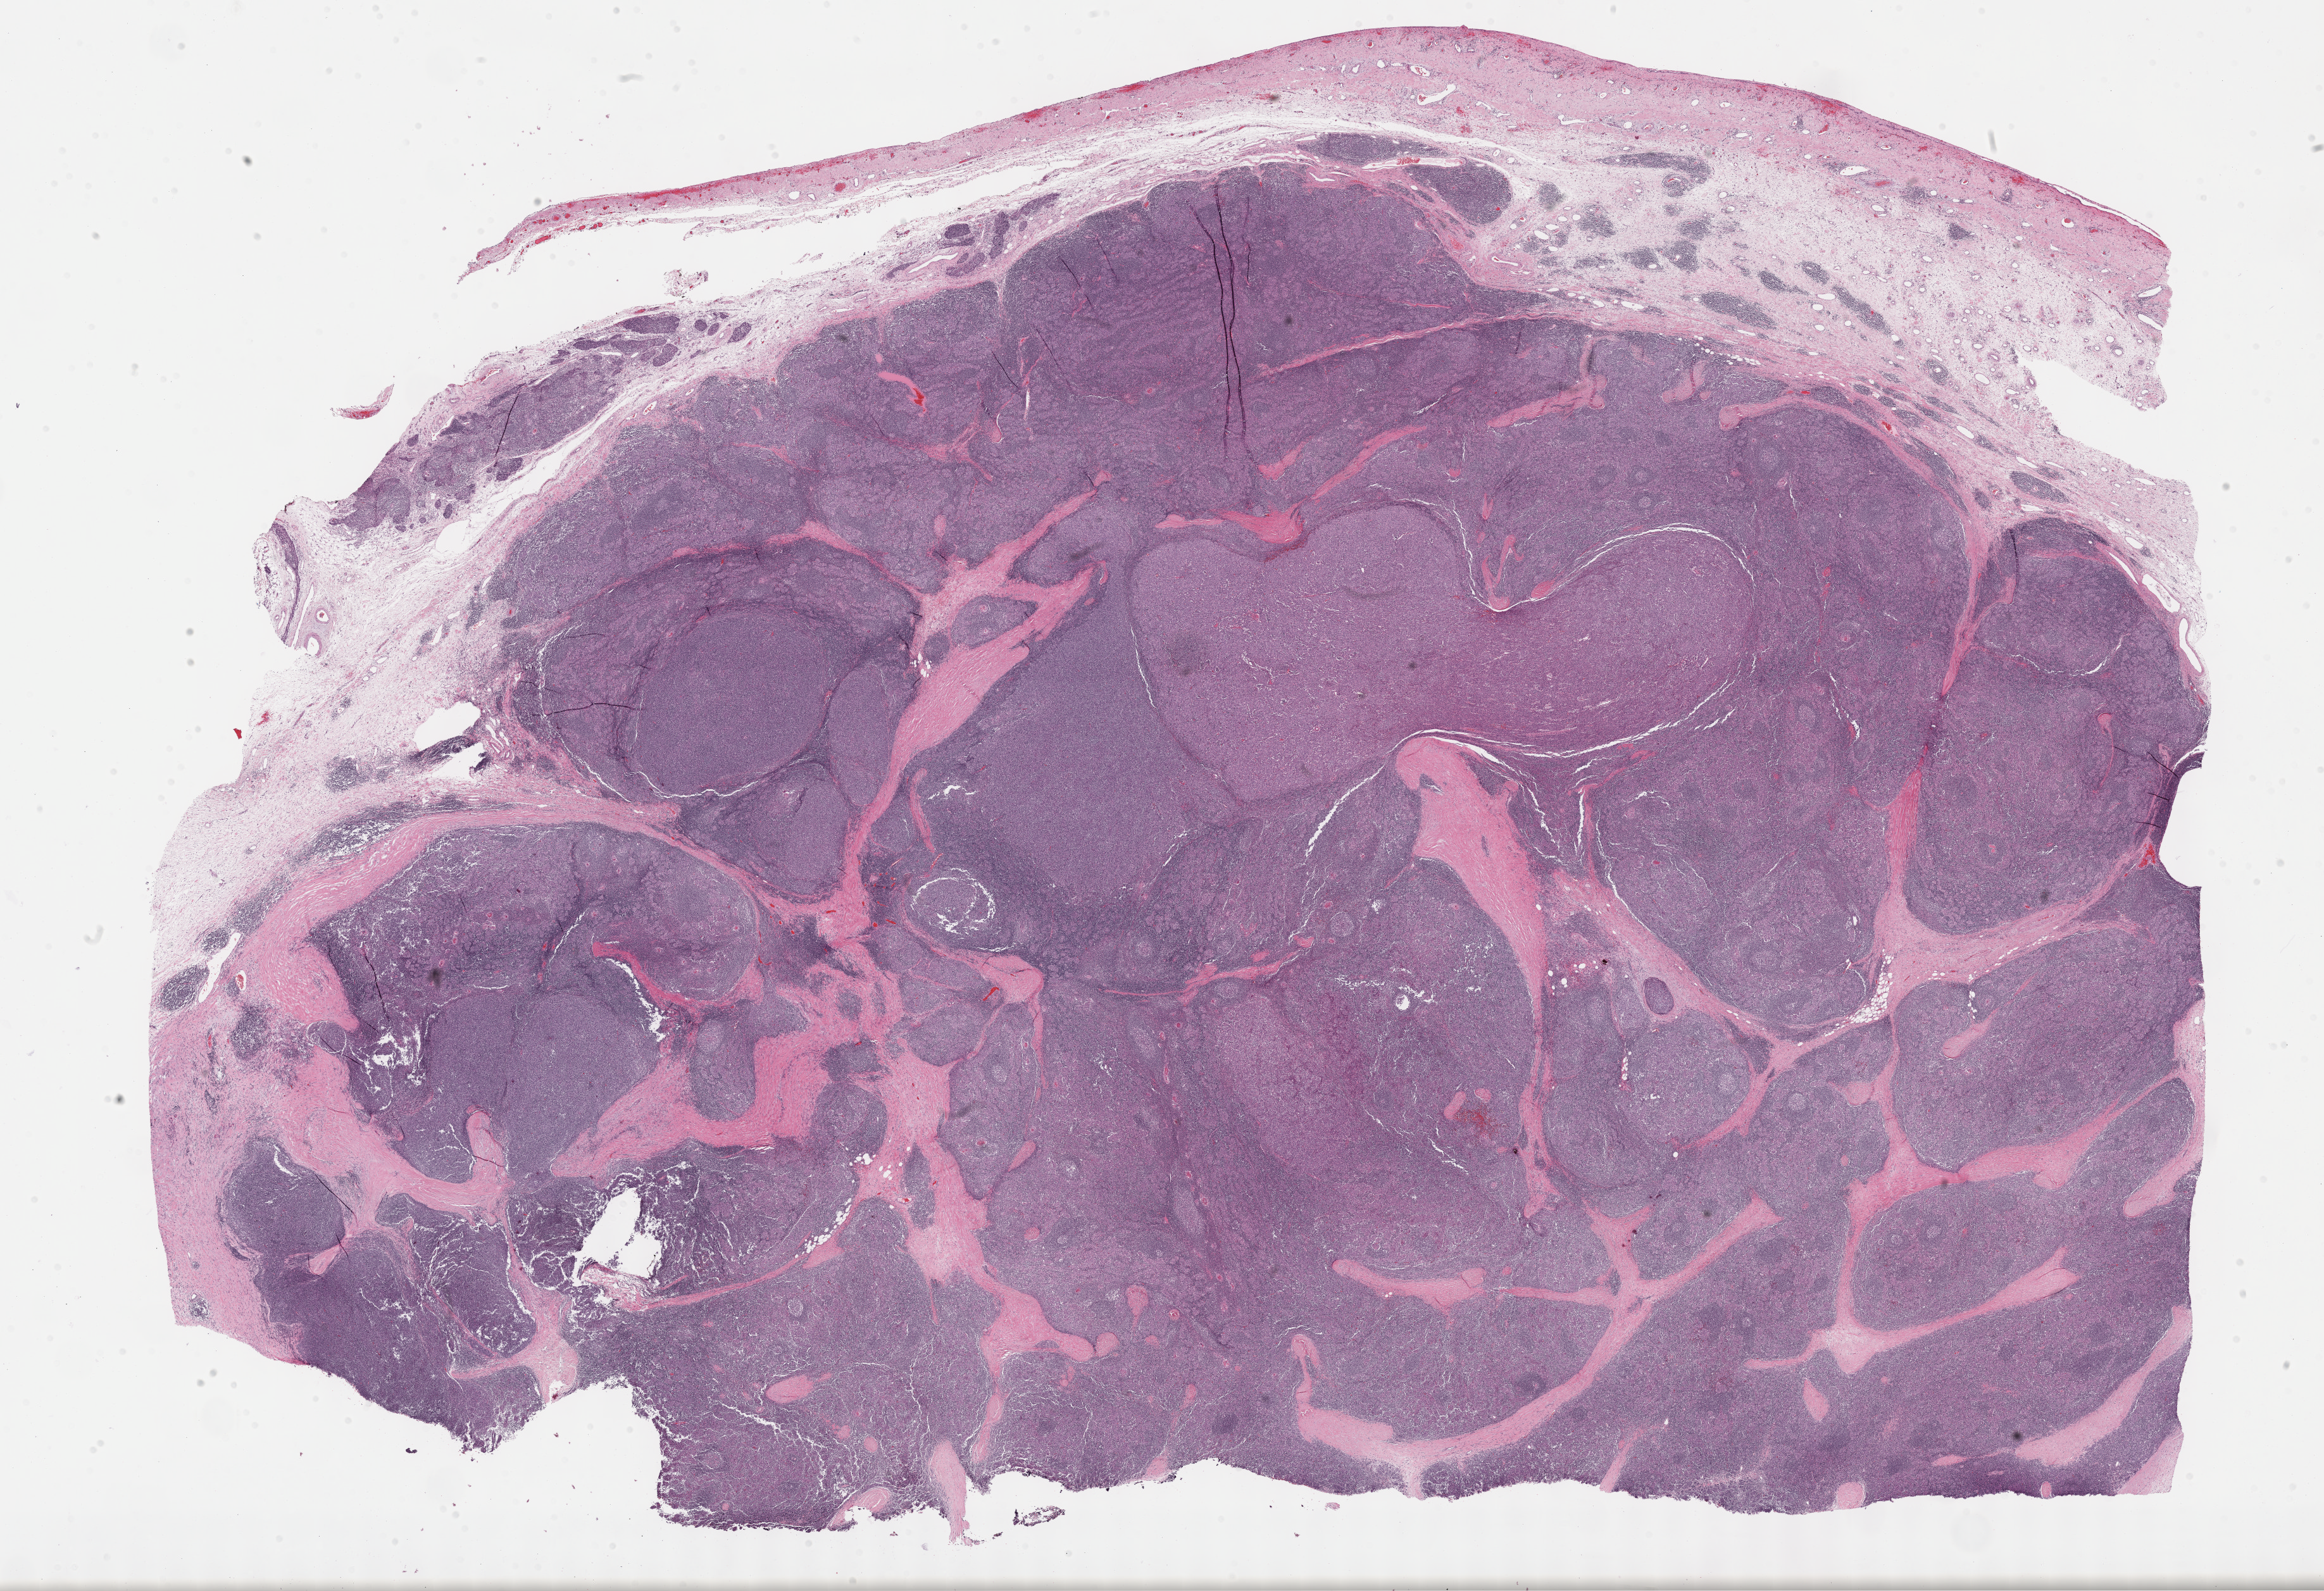
Whole-slide histology image, H&E, whole scanned area (about 29.7 x 20.3 mm, slide scanned at 40x) shown as a low-resolution overview, FFPE section, thymus, primary tumour sample. Female, age 71 years at initial diagnosis.
- pathologic diagnosis: Thymoma, type A, malignant (anterior mediastinum)